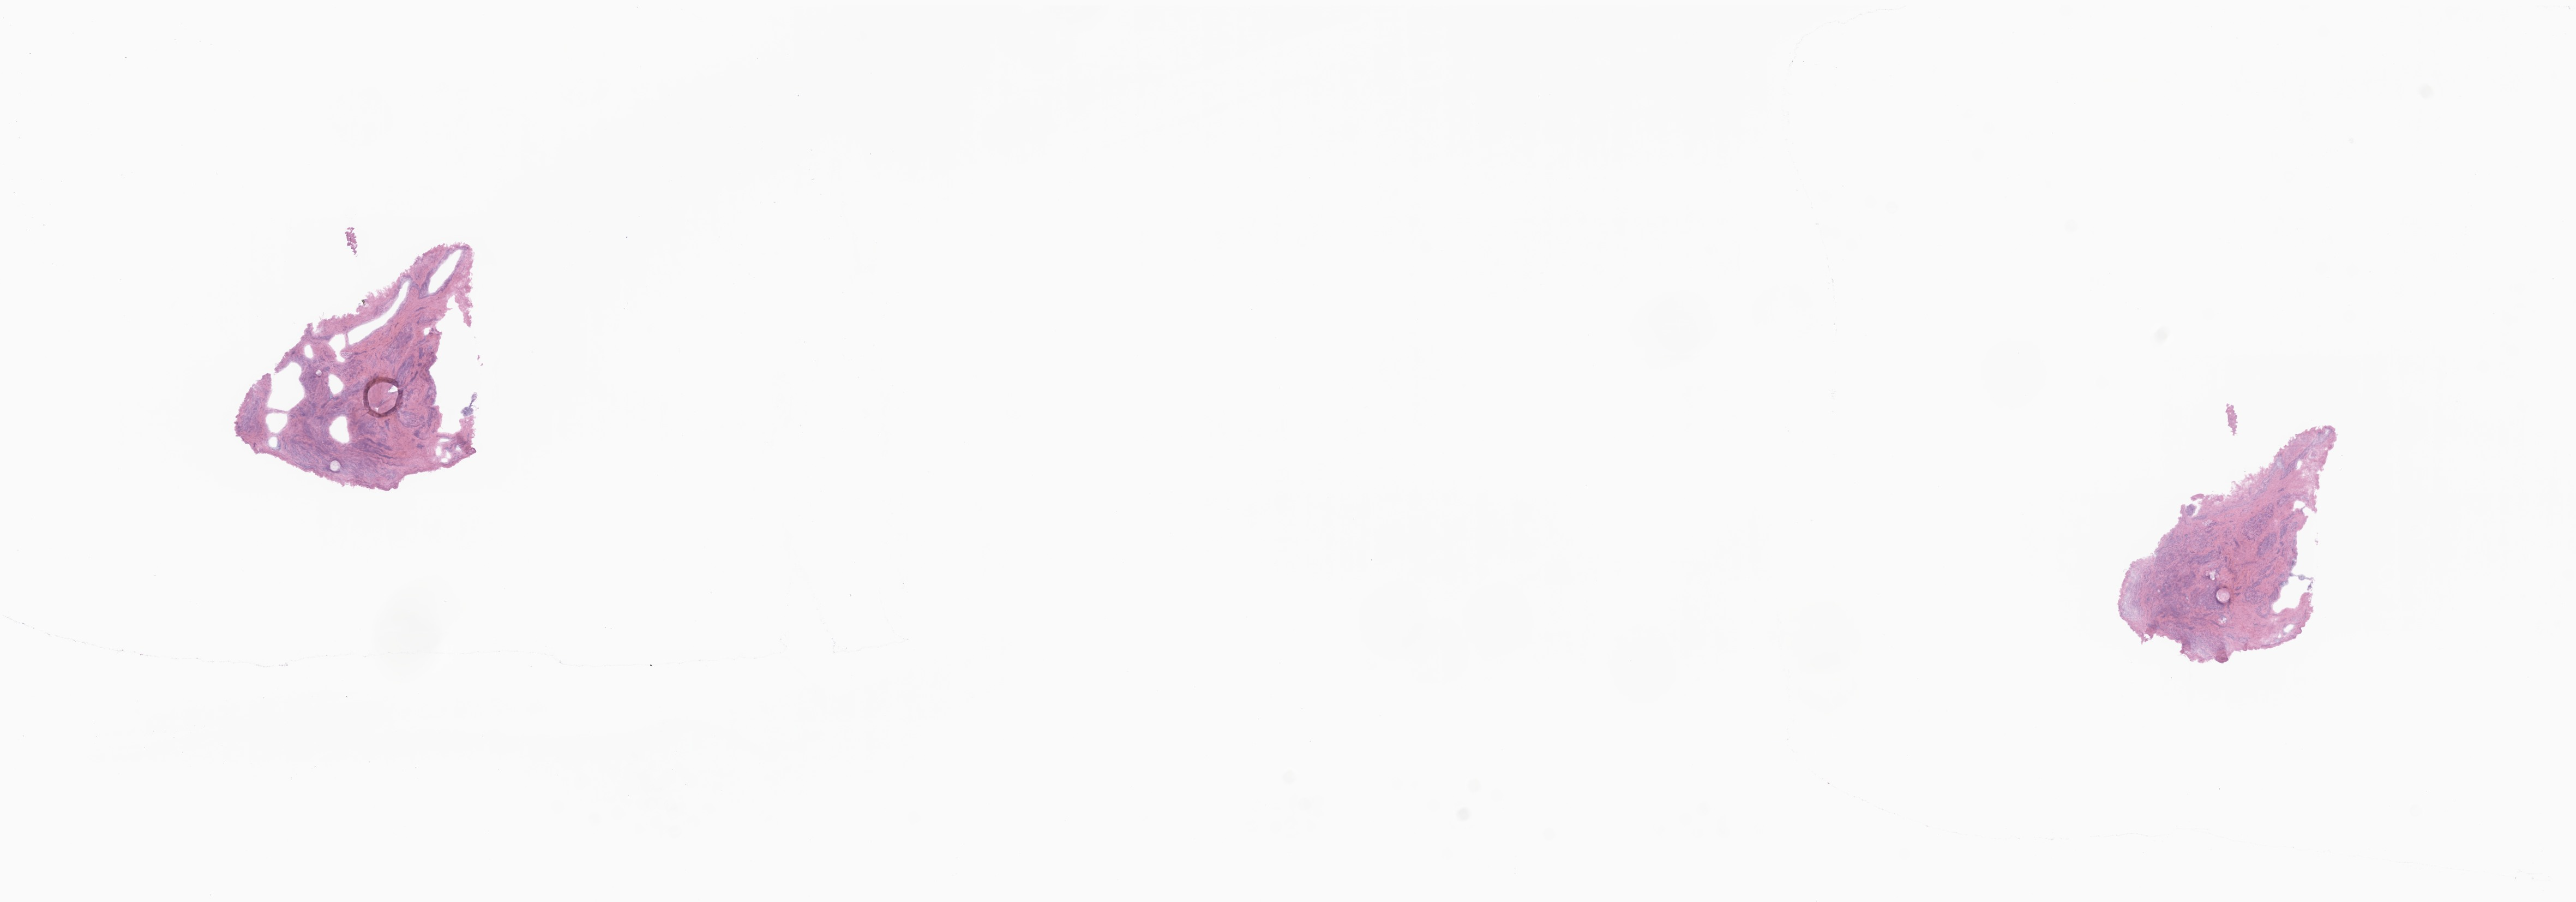
Digitized hematoxylin and eosin (H&E)-stained section, shown as a low-resolution overview of the whole scanned area (about 19.9 x 7.0 mm). Frozen section. Specimen: normal-tissue sample (non-tumor) from a patient with serous borderline tumor, NOS. Anatomic site: uterine adnexa. Patient sex: female. Slide review estimates, as recorded: tumor cells 0%, tumor nuclei 0%, stromal cells 100%, necrosis 0%, normal cells 0%. Infiltration values recorded for this section: lymphocyte infiltration 0%, monocyte infiltration 0%, neutrophil infiltration 0%.
* this section: non-tumor tissue sample; the patient's diagnosis is given above
* section: top of the tissue portion